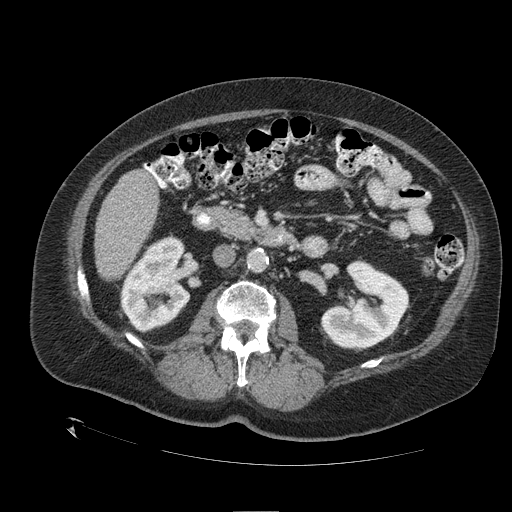
Contrast-enhanced abdominal CT (liver protocol), one axial slice. Position 43 of 109 along the scan axis. 120 kVp. One of 2 acquisitions stored at this slice position. Soft-tissue window (W 400 / L 40 HU). 2.5 mm slice thickness. 512 × 512 image matrix, field of view 460 × 460 mm. Case-level facts recorded for this patient, not image findings: diagnosis: hepatocellular carcinoma (patient treated with transarterial chemoembolisation; whether this scan precedes or follows treatment is not stated here); TNM stage (as recorded): Stage-I; Child-Pugh class: A; tumour differentiation: no biopsy; tumour nodularity: uninodular.
Outlined on this slice (semi-automatic segmentation, software-assisted and operator-edited):
- liver parenchyma outside the tumour (the mass and vessels are separate outlines, so this box may not span the whole liver): bounding box [x1, y1, x2, y2] px = [94, 167, 158, 280]
- liver vessels: [146, 168, 150, 171]